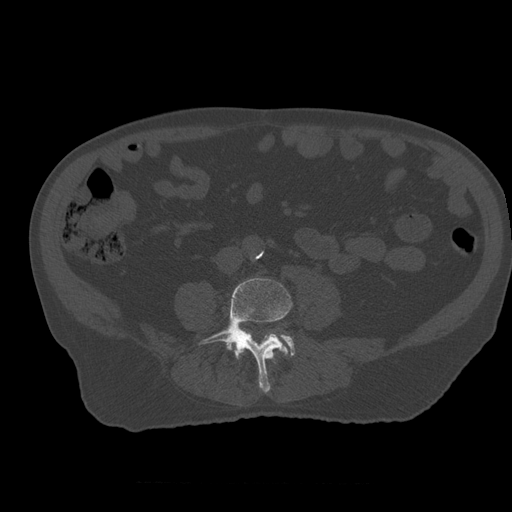
CT including the spine, one axial slice; position 163 of 399 along the scan axis; reconstruction kernel STANDARD; 120 kVp; bone window (W 1800 / L 400 HU); 1.25 mm slice thickness; 512 × 512 image matrix, field of view 407 × 407 mm. Patient age 73 years. Case-level facts recorded for this patient, not image findings: primary cancer: prostate; vertebrae with lytic lesions (as recorded): L2.
Annotated regions visible in this slice (semi-automatic segmentation, software-assisted and operator-edited):
- L3 vertebra: bounding box (x1, y1, x2, y2) in pixels: (272, 351, 275, 363)
- L4 vertebra: (199, 278, 292, 392)
- L5 vertebra: (281, 335, 296, 356)